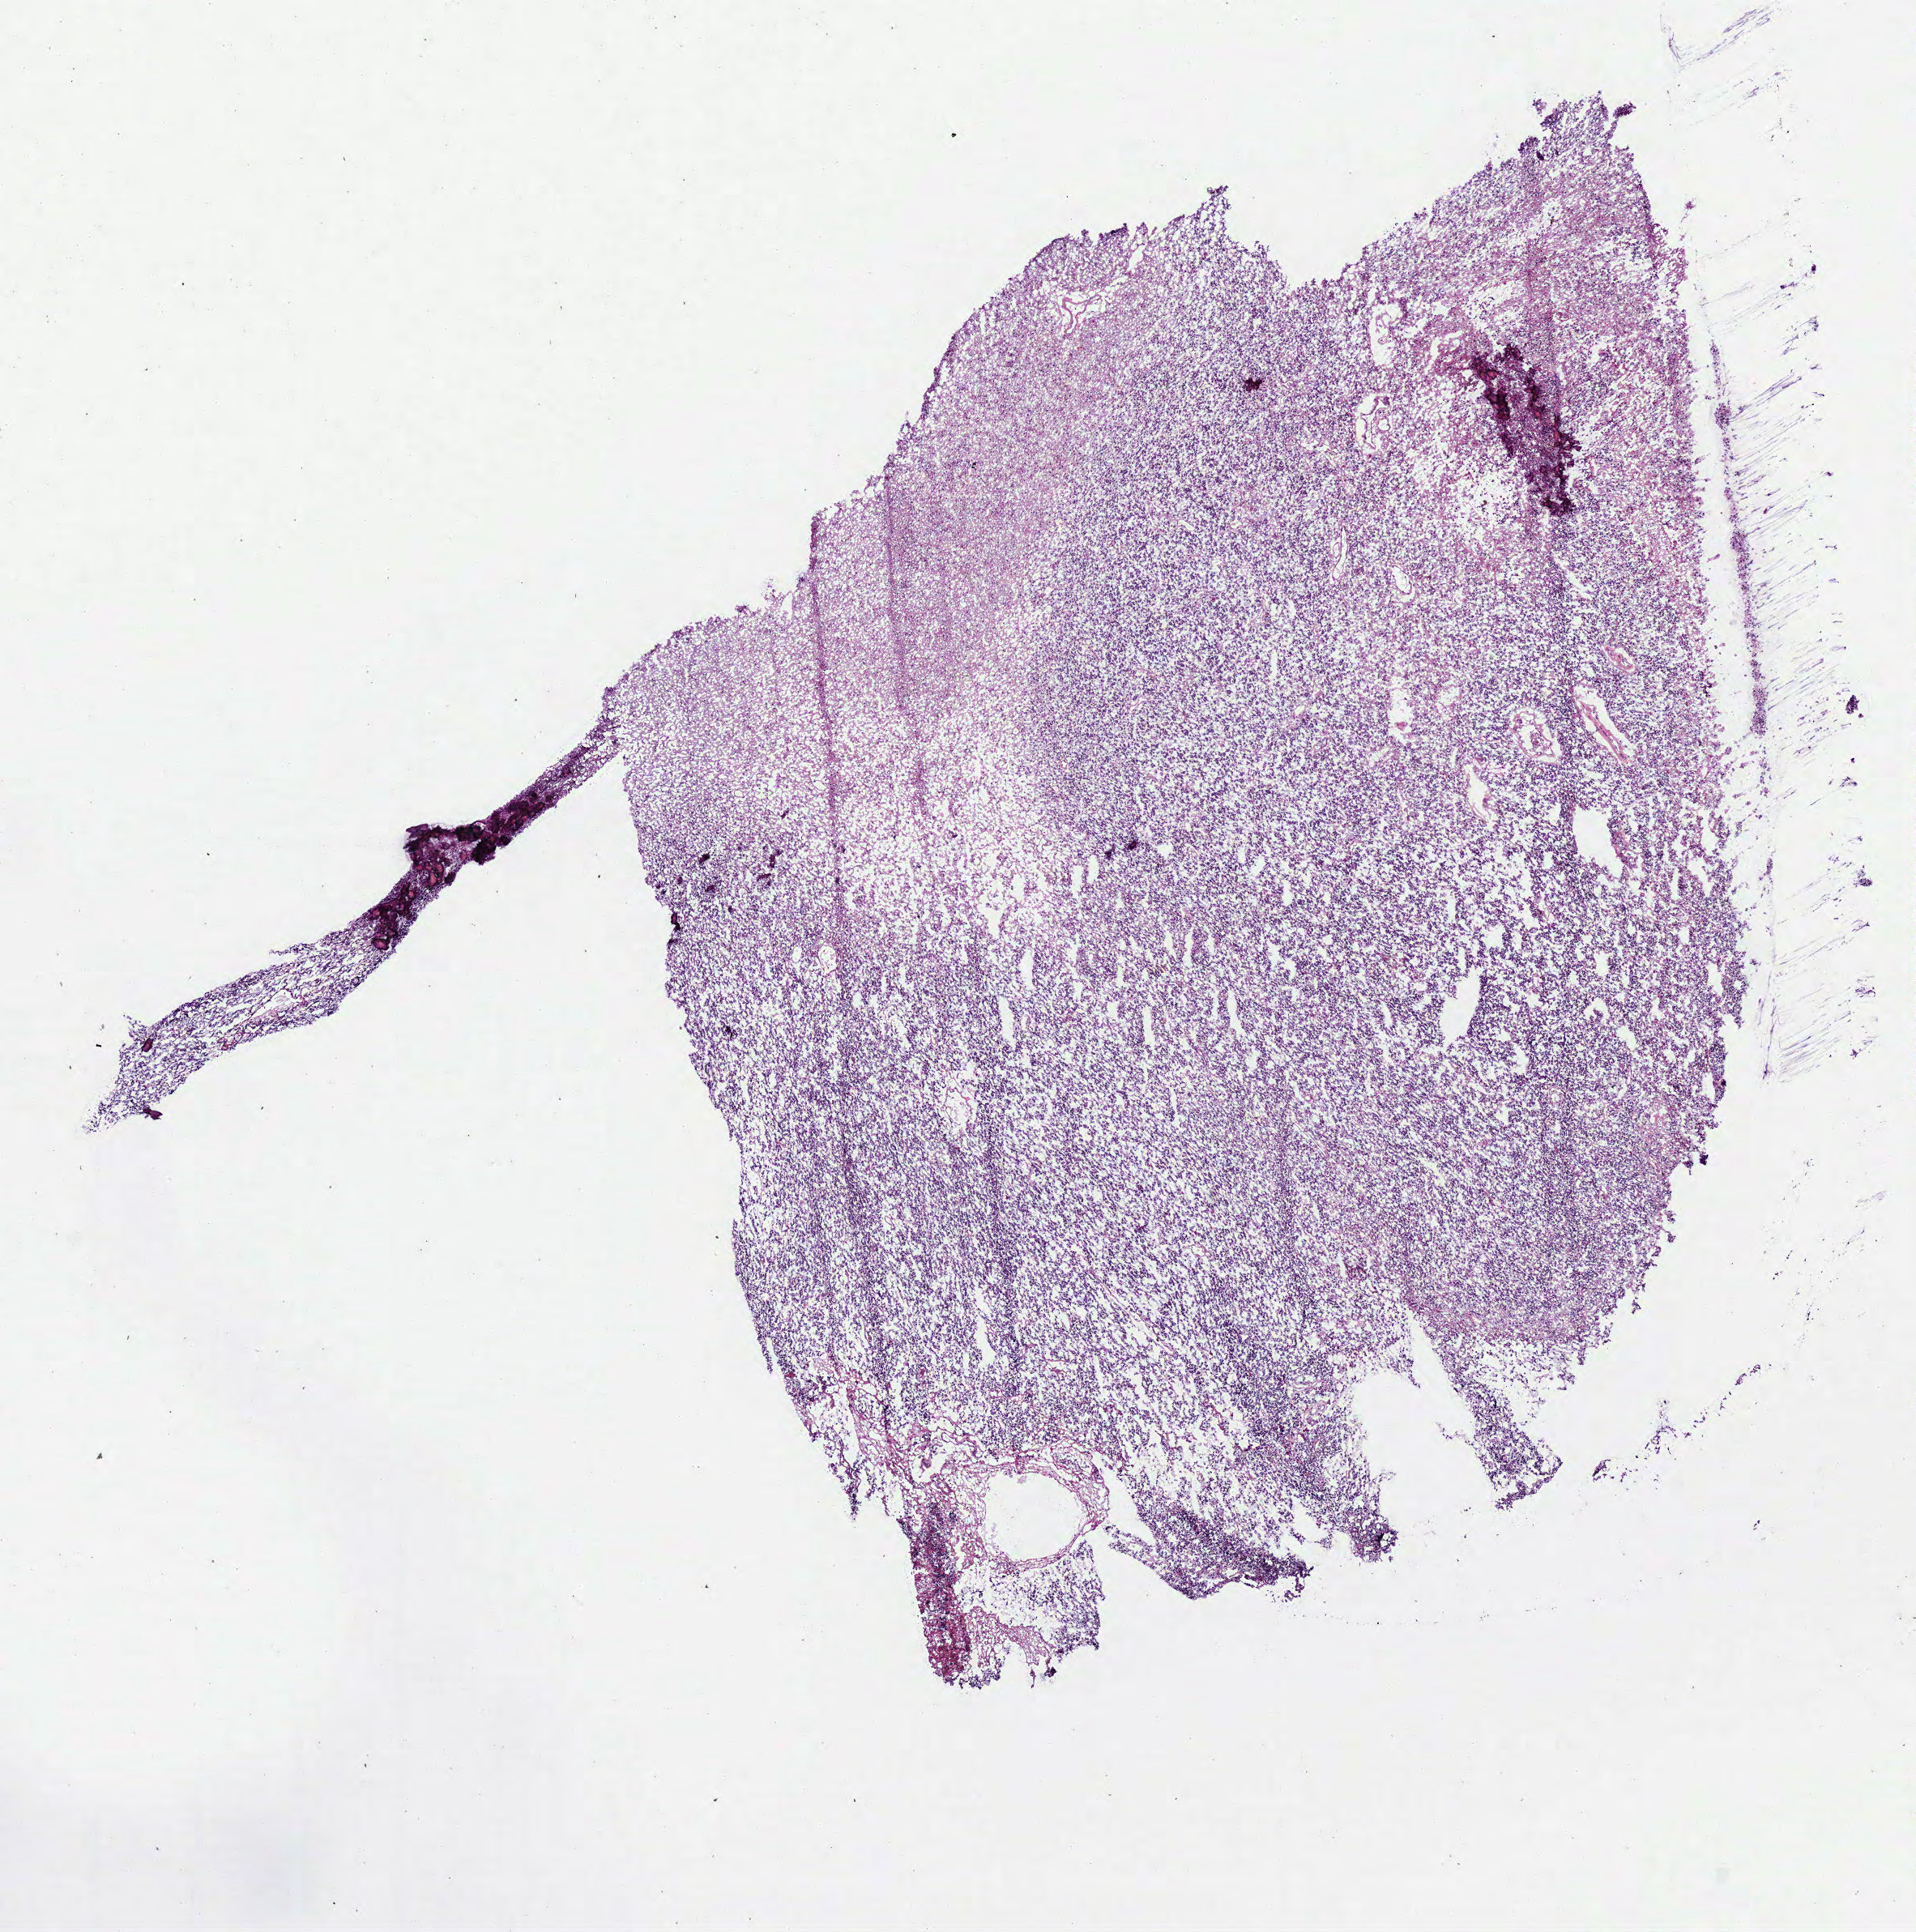
Digitized H&E-stained tissue section (whole slide), low-resolution overview of the scanned area, about 9.3 x 9.4 mm (acquisition: 40x scan), frozen section from the bottom of the tissue portion, sample: primary tumour, brain. Male, age 66 years at initial diagnosis. Histologic grade: G3 (poorly differentiated). Pathologist review of this section (percent, as recorded): tumour cells 100%, tumour nuclei 80%, normal cells 0%, stromal cells 0%, necrosis 0%.
- histologic diagnosis: Oligodendroglioma, anaplastic (cerebrum)